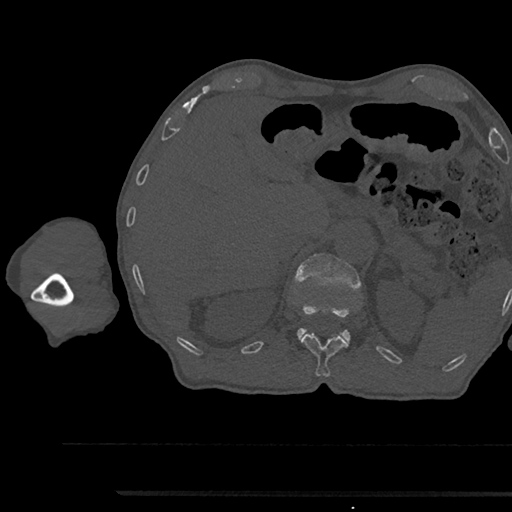
CT including the spine, one axial slice; position 684 of 797 along the scan axis; reconstruction kernel Br40s/3; 120 kVp; bone window (W 1800 / L 400 HU); 0.5 mm slice thickness; 512 × 512 image matrix, field of view 367 × 367 mm. Male patient, age 79 years. From the clinical record (not read from this slice): primary cancer: prostate.
Annotated regions visible in this slice (semi-automatically segmented with operator editing):
- L1 vertebra: bounding box (x1, y1, x2, y2) in pixels: (294, 254, 361, 342)
- T12 vertebra: (301, 333, 349, 377)